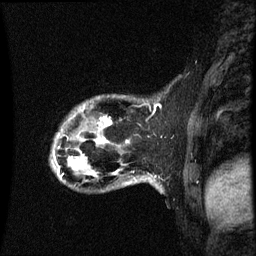
Breast MRI (dynamic contrast-enhanced), one sagittal slice. Slice 12 of 60 in the series (ordered by position). Dynamic contrast-enhanced series, image 2 of 3 at this slice position (ordered by acquisition). 1.5 T. TE 4.2 ms, TR 8.9 ms. 2 mm slice thickness. 256 × 256 image matrix. Female patient, age 44 years. Case-level facts recorded for this patient, not image findings: setting: breast cancer imaged before/during neoadjuvant chemotherapy; receptor status: HR-positive, HER2-negative.
Annotated regions visible in this slice (semi-automatic segmentation, software-assisted and operator-edited):
- analysis volume of interest (the breast-tissue region the enhancement analysis was run in; not a lesion): bounding box [x1, y1, x2, y2] px = [51, 96, 153, 185]
- tumour enhancement mask (voxels above the 70 % enhancement threshold inside the analysis volume of interest): [68, 122, 111, 171]